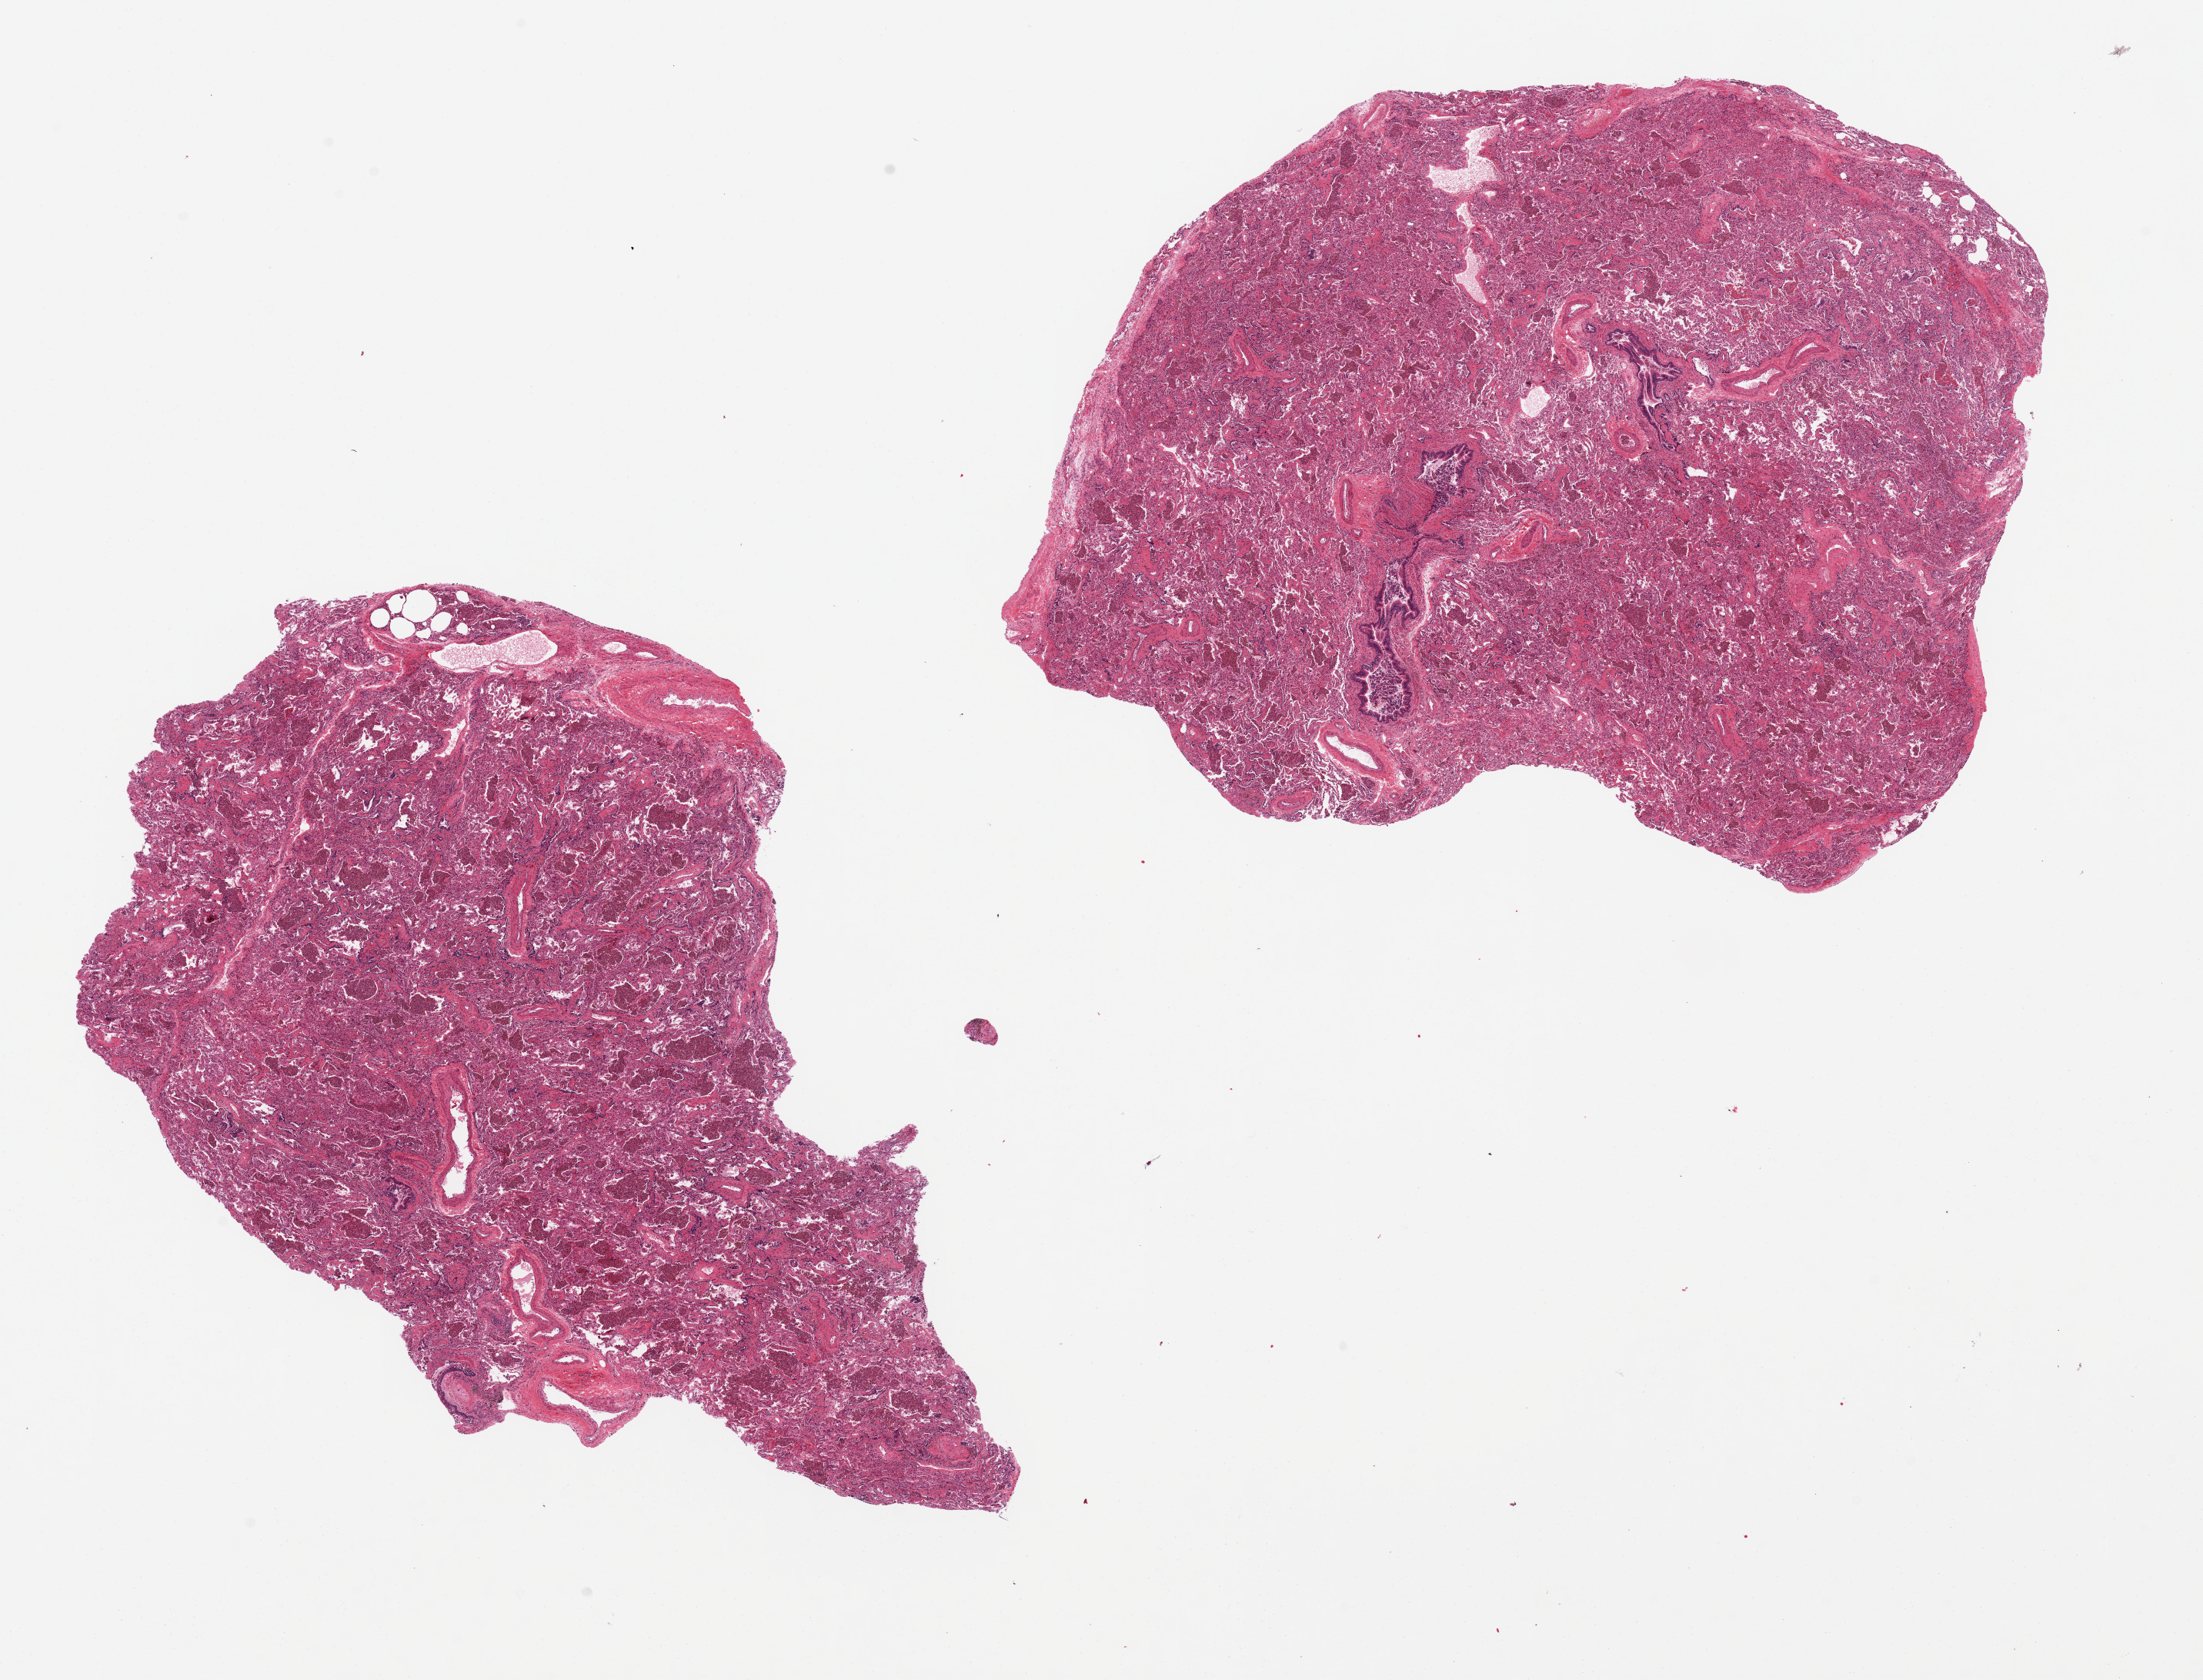
H&E whole-slide image, low-resolution overview of the scanned area, about 22.6 x 17.3 mm. PAXgene-fixed, paraffin-embedded tissue. Sampled site (target tissue): lung. Donor tissue sample. Donor sex: female.
Review note (as recorded): 2 pieces, dense congestion, hemosiderin laden macrophages distending alveoli; fibrin deposition.